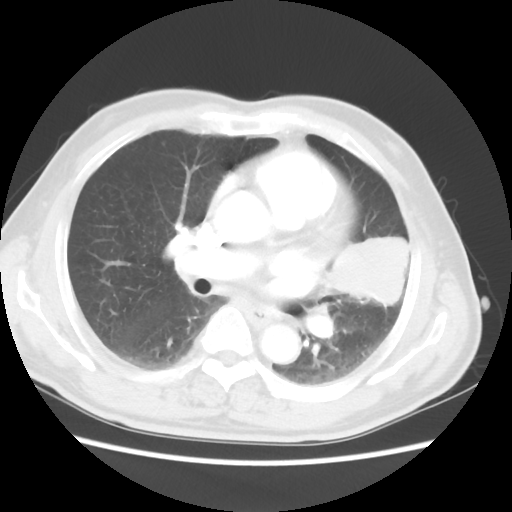
Chest CT, one axial slice; position 27 of 50 along the scan axis; reconstruction kernel STANDARD; 120 kVp; lung window (W 1500 / L -600 HU); 5 mm slice thickness; 512 × 512 image matrix. Male patient, age 69 years. From the clinical record (not read from this slice): clinical TNM (as recorded): T3 N1 M1a.
Outlined on this slice (rectangle marked by the reading radiologist):
- lung tumour (recorded histology: squamous cell carcinoma): box from (x=315, y=208) to (x=415, y=315) px